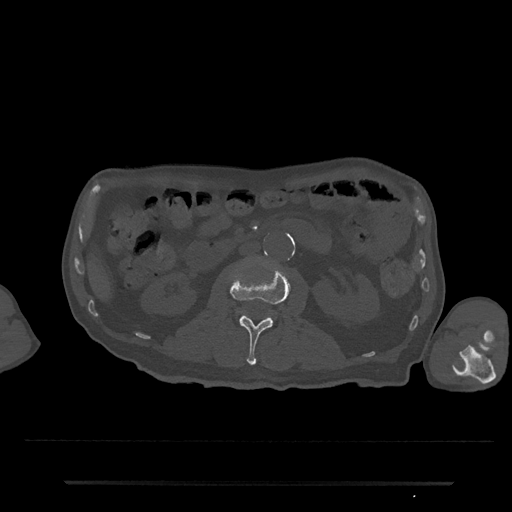
CT including the spine, one axial slice; slice 40 of 797 in the series (ordered by position); 120 kVp; bone window (W 1800 / L 400 HU); 512 × 512 image matrix. Patient: male, 74 years. Case-level facts recorded for this patient, not image findings: primary cancer: prostate.
Outlined on this slice (semi-automatically segmented with operator editing):
- L2 vertebra: bounding box (x1, y1, x2, y2) in pixels: (230, 266, 291, 365)
- L3 vertebra: (236, 308, 277, 318)